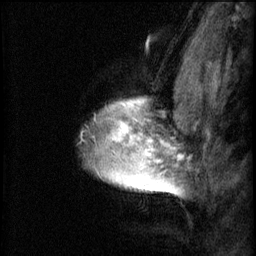
Breast MRI (dynamic contrast-enhanced), one sagittal slice; slice 51 of 60 in the series (ordered by position); 3 images stored at this slice position (order not interpretable as contrast timing); 1.5 T; TE 4.2 ms, TR 8.2 ms; 256 × 256 image matrix, field of view 180 × 180 mm. Patient: female, 40 years.
Structures marked on this image (semi-automatically segmented with operator editing):
- analysis volume of interest (the breast-tissue region the enhancement analysis was run in; not a lesion): bounding box (x1, y1, x2, y2) in pixels: (85, 84, 167, 193)
- tumour enhancement mask (voxels above the 70 % enhancement threshold inside the analysis volume of interest): (95, 100, 167, 193)